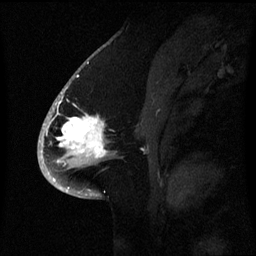
Breast MRI (dynamic contrast-enhanced), one sagittal slice; slice 37 of 60 in the series (ordered by position); dynamic contrast-enhanced series, image 2 of 3 at this slice position (ordered by acquisition); 1.5 T; TE 4.2 ms, TR 8.4 ms; 2.1 mm slice thickness; 256 × 256 image matrix, field of view 220 × 220 mm. Patient: female, 53 years. From the clinical record (not read from this slice): setting: breast cancer imaged before/during neoadjuvant chemotherapy; receptor status: HR-positive, HER2-negative.
Outlined on this slice (semi-automatic segmentation, software-assisted and operator-edited):
- analysis volume of interest (the breast-tissue region the enhancement analysis was run in; not a lesion): box from (x=52, y=90) to (x=124, y=171) px
- tumour enhancement mask (voxels above the 70 % enhancement threshold inside the analysis volume of interest): (x=57, y=90)–(x=108, y=163)